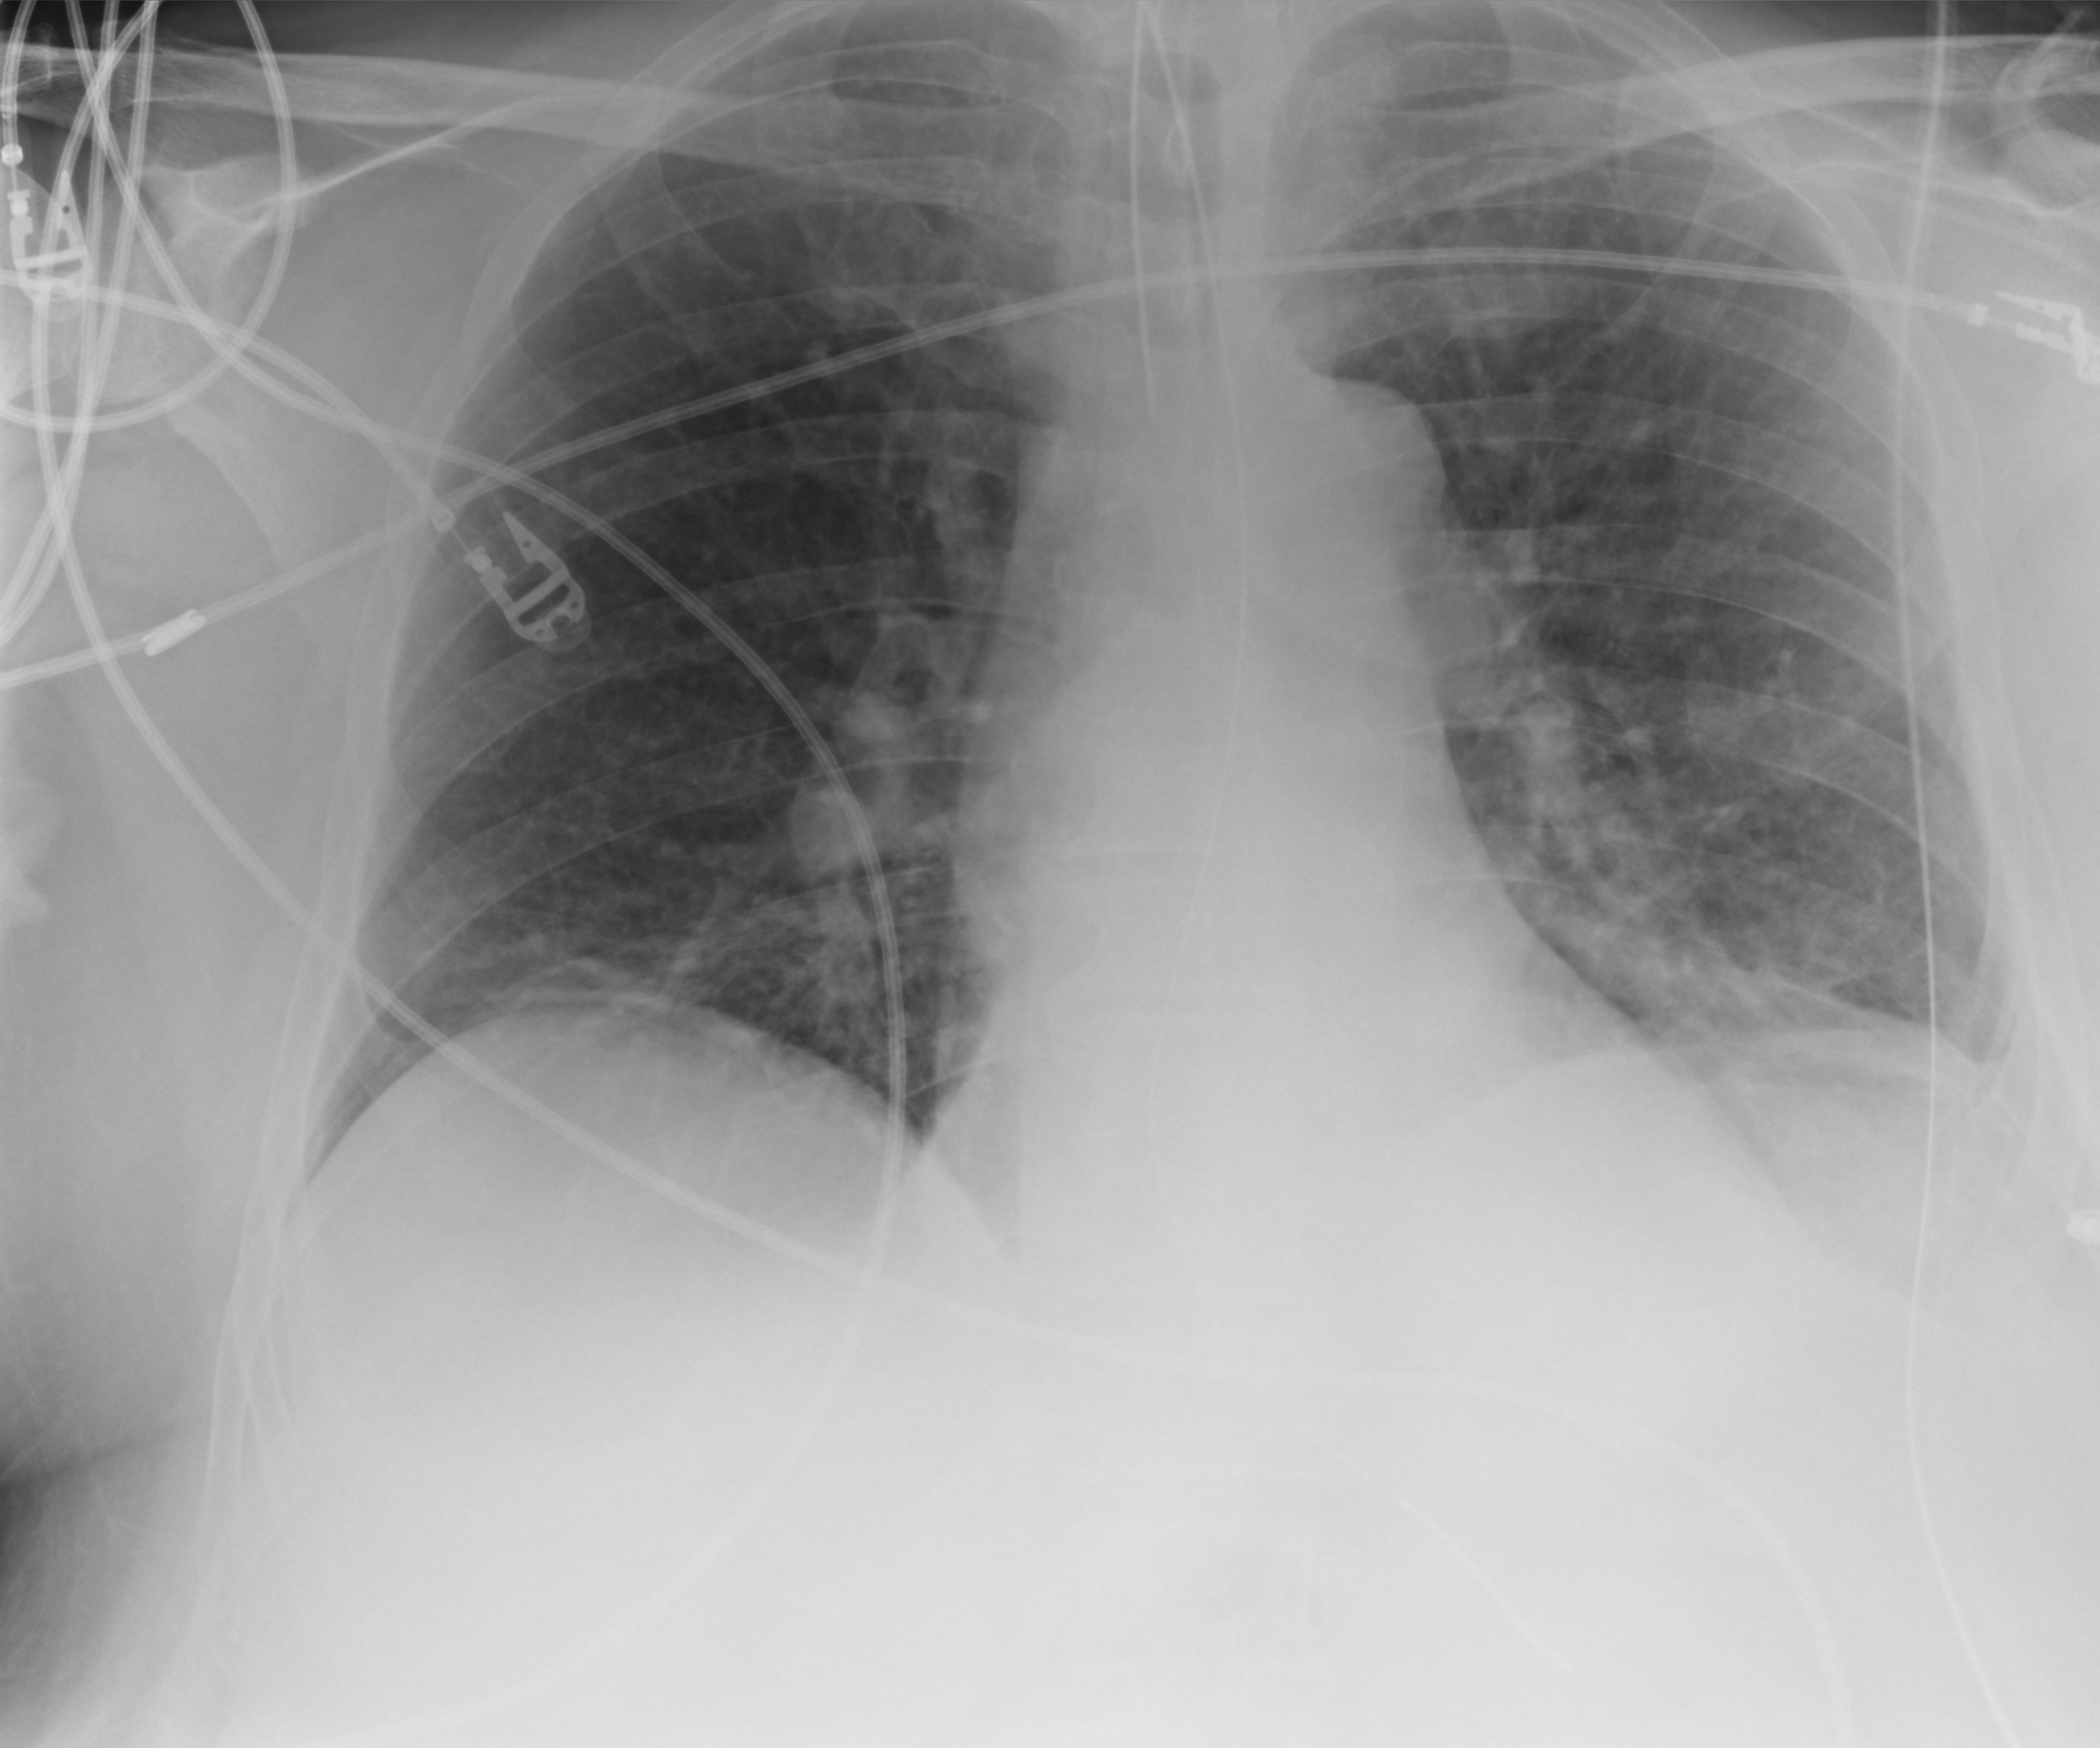
Bedside chest radiograph (computed radiography); anteroposterior (AP) projection. Male patient hospitalised with COVID-19, age 60–74 years.
From the hospital-stay record, not from the radiograph (when in the stay this image was taken is not recorded):
- admitted to intensive care during this hospital stay: yes
- length of hospital stay: 22 days
- mechanically ventilated during this hospital stay: yes